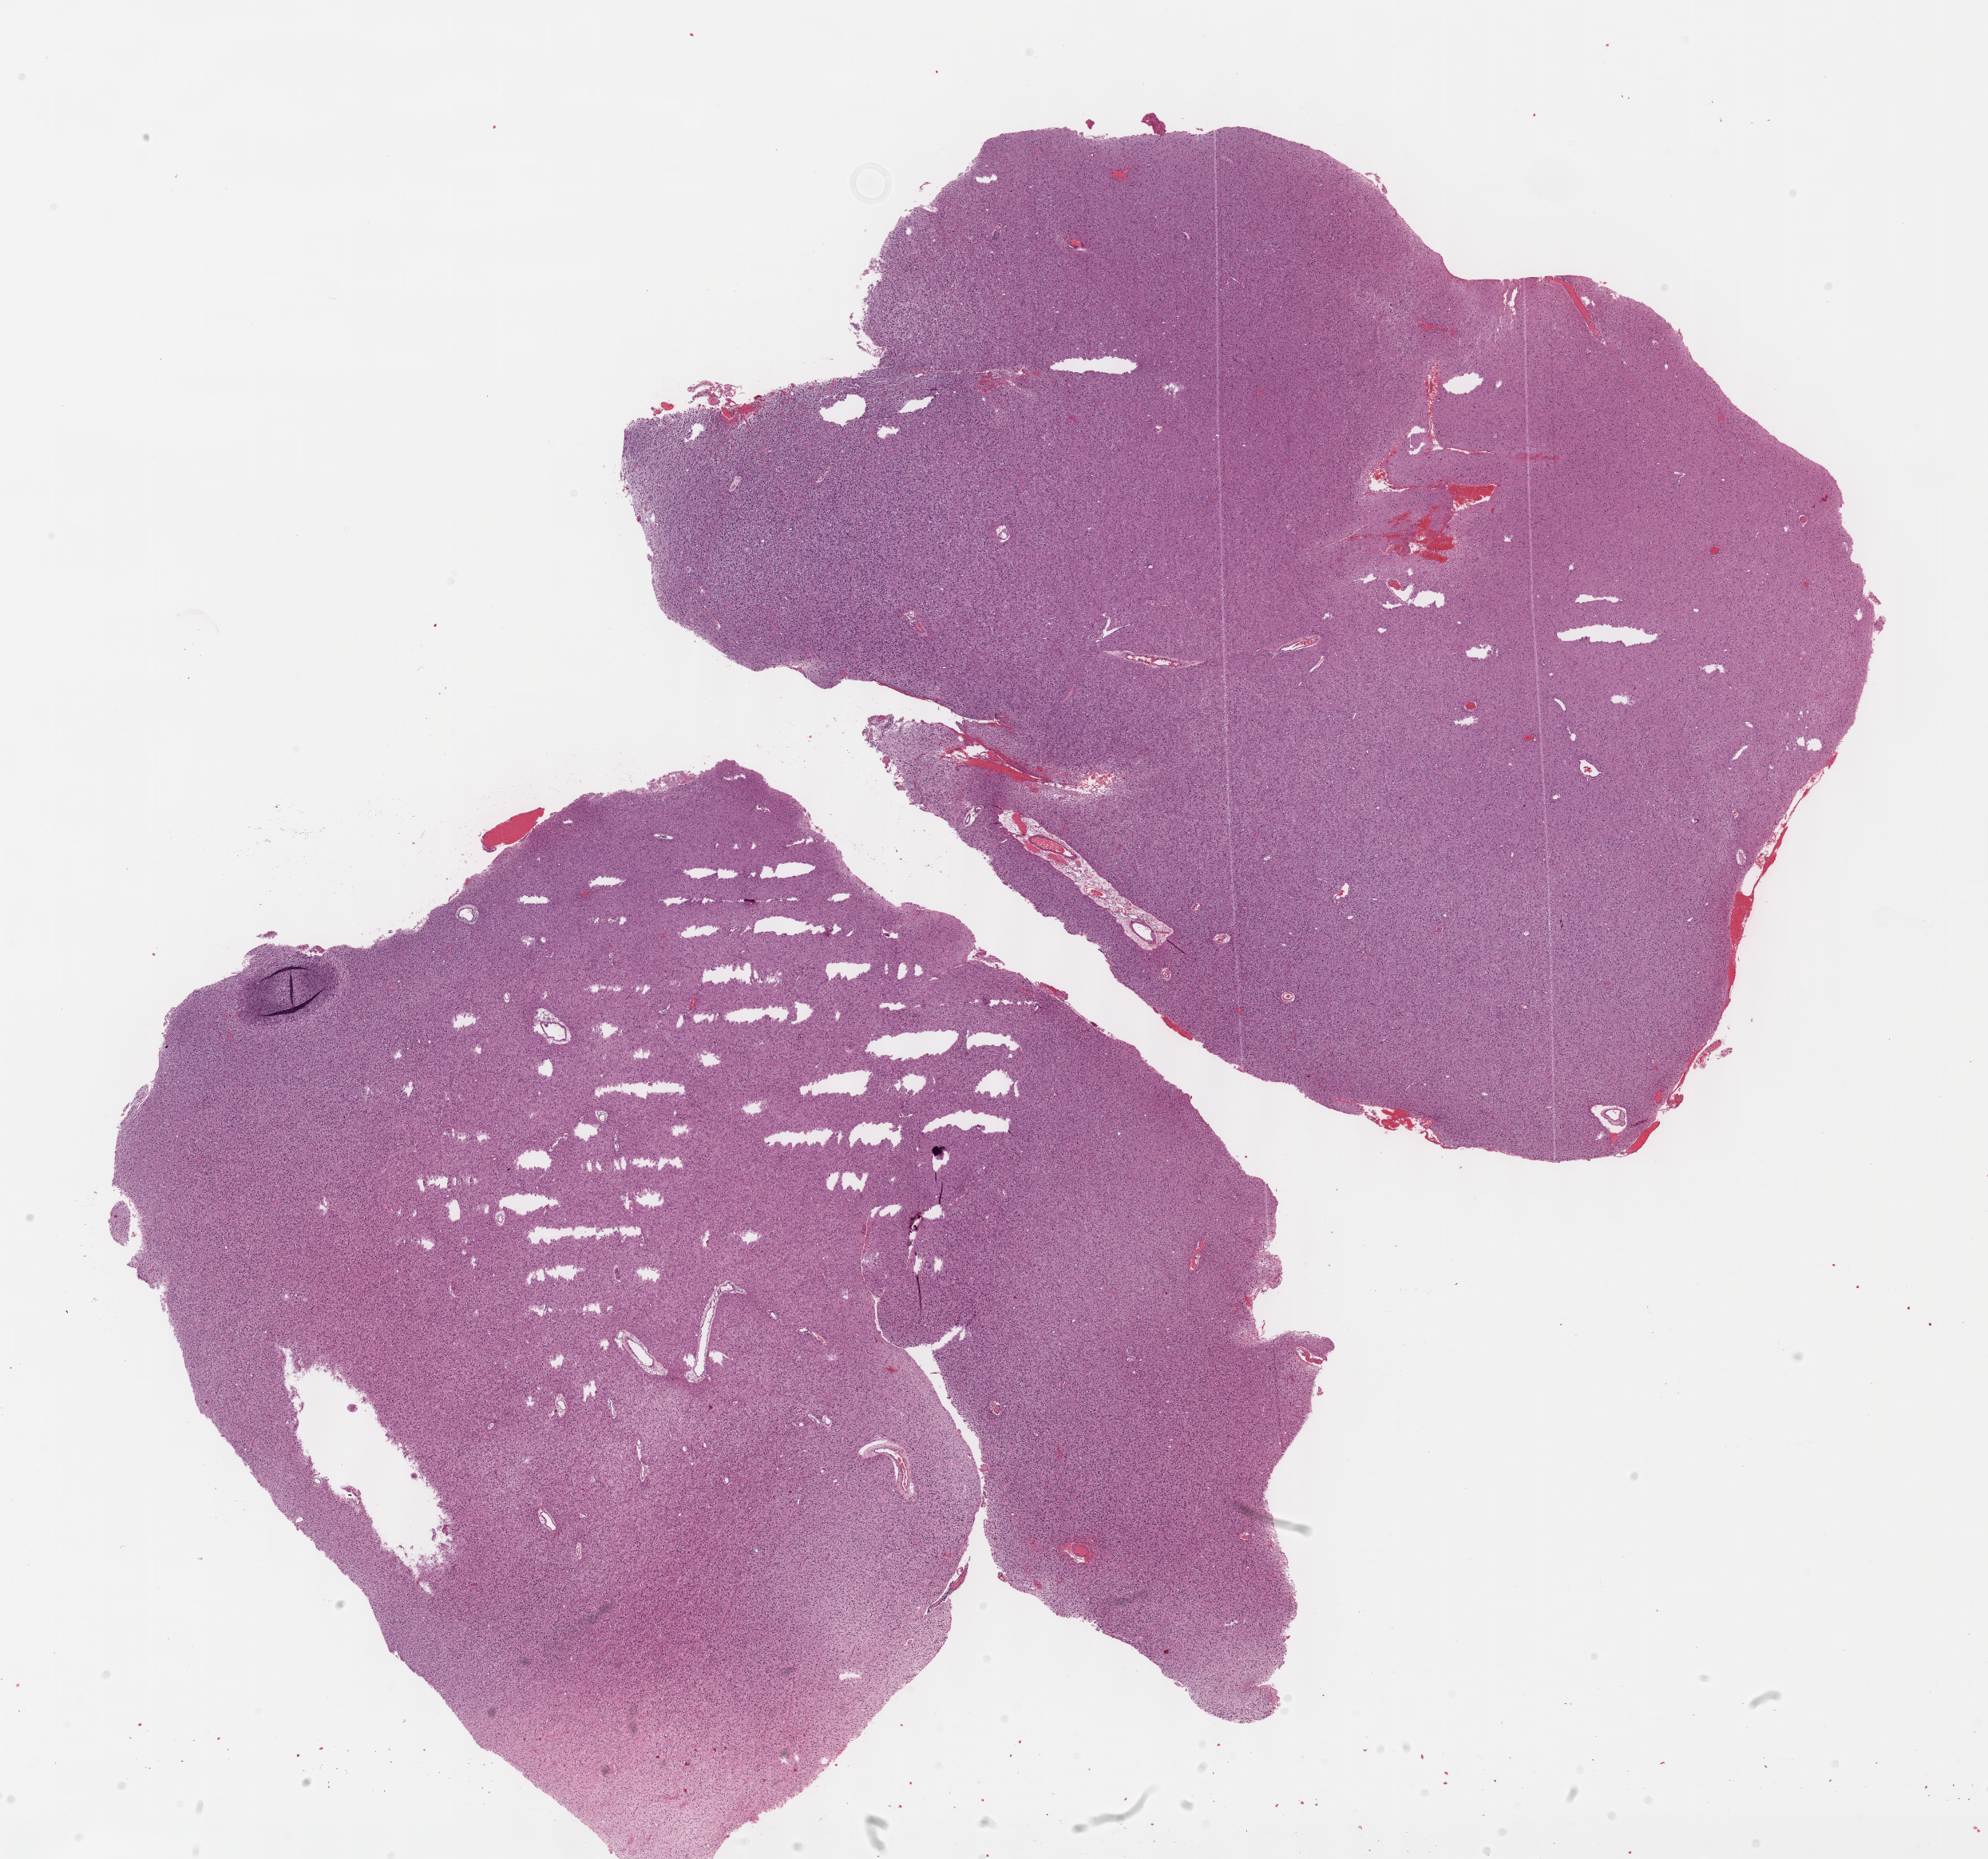
Digitized H&E-stained tissue section (whole slide), shown as a low-resolution overview of the whole scanned area (about 20.1 x 18.8 mm). Formalin-fixed paraffin-embedded (FFPE) diagnostic section. Primary tumour sample from the brain. Male patient; age at initial diagnosis 36 years. Histologic grade: G3 (poorly differentiated).
* diagnosis: Mixed glioma (cerebrum)